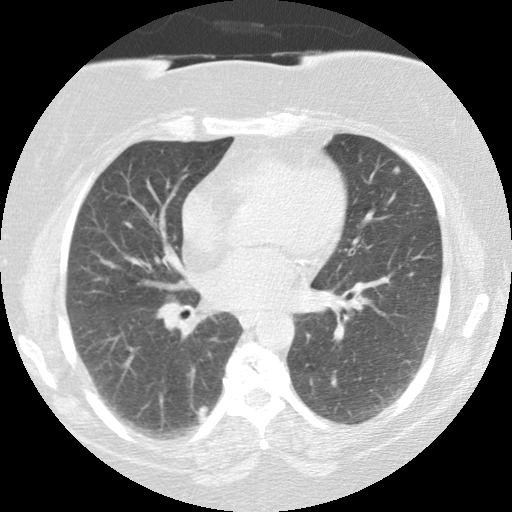
Low-dose screening chest CT, axial slice; first (baseline) screen; lung window (W 1500 / L -600 HU); 2.5 mm slice thickness; 140 kVp; slice 55 of 111 in the series; 512 × 512 image matrix, field of view 316 × 316 mm. Female, age 58 years at enrolment. Current smoker at enrolment.
- Expert reader's lesion annotation, bounding box [x1, y1, x2, y2] px = [176, 392, 226, 442].
- The screening reader recorded 4 non-calcified nodules or masses ≥4 mm on this exam (left lower lobe, lingula, right middle lobe, right upper lobe); which of them this box marks is not recorded.
- Official screen result: positive, change unspecified: nodule(s) >= 4 mm or enlarging nodule(s), mass(es), or other non-specific abnormalities suspicious for lung cancer.
- Participant outcome: lung cancer diagnosed 644 days after this screen — adenocarcinoma, NOS, right lower lobe, stage IIIA (AJCC 6th edition), 25 mm at pathology.